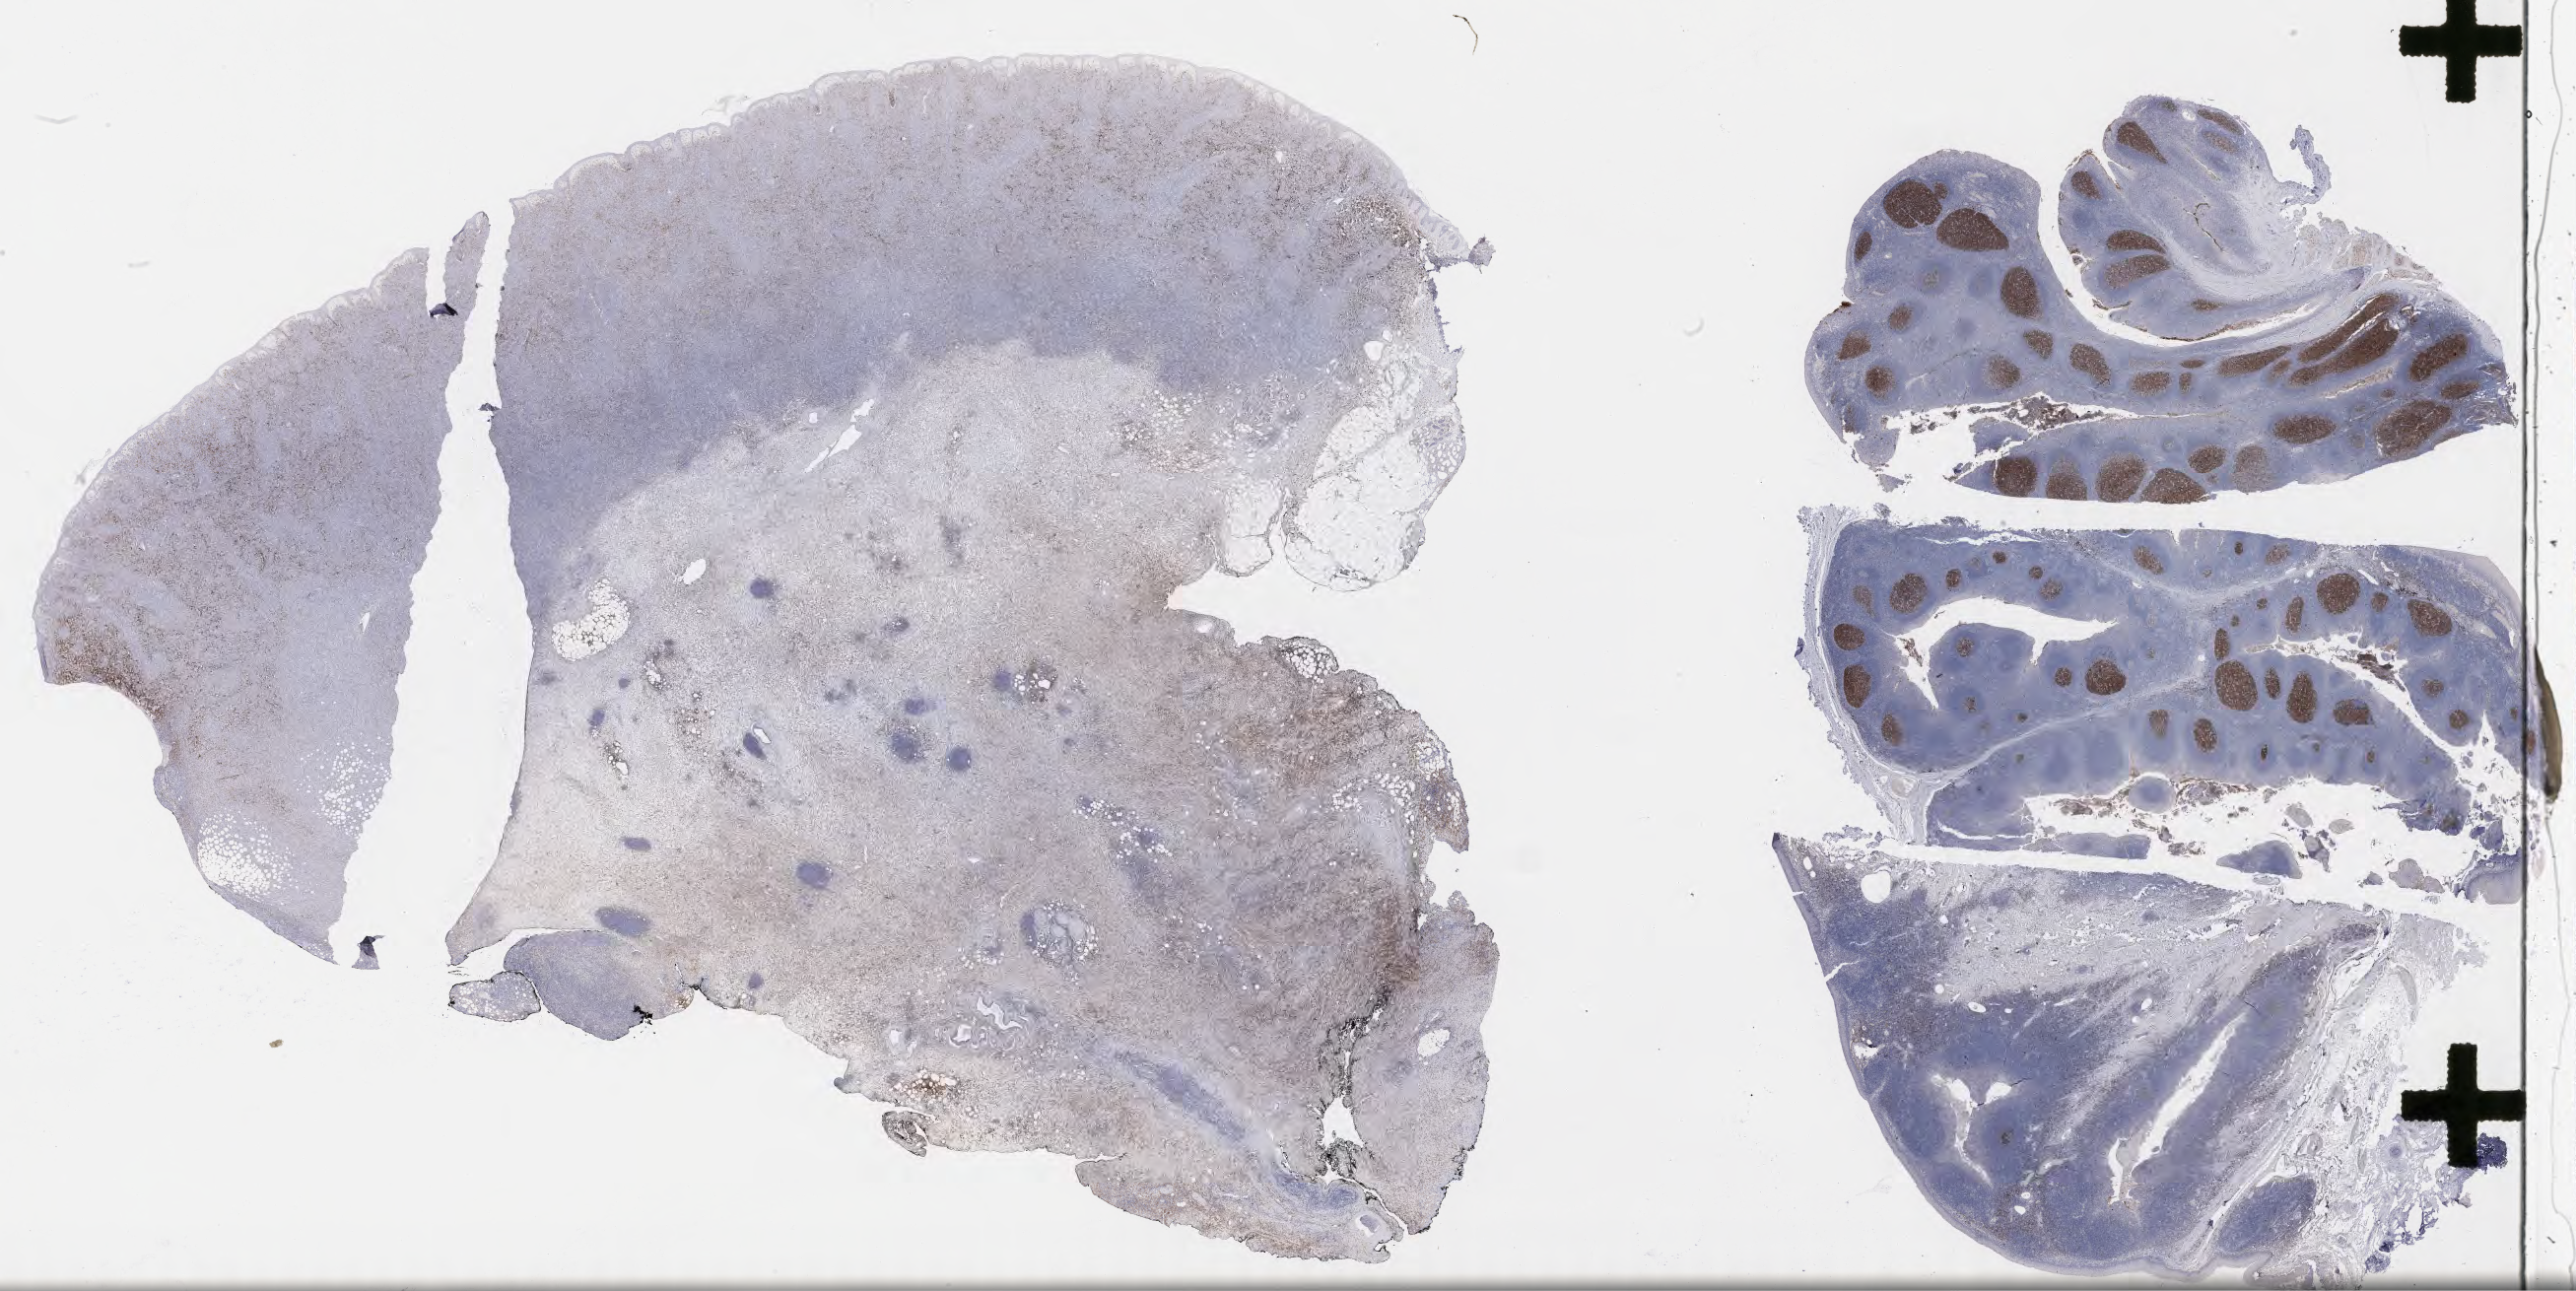
Immunohistochemistry (IHC) whole-slide image stained for CD10 — low-resolution overview of the scanned area, about 42.3 x 21.2 mm, specimen: tumor tissue, anatomic site: lymph node. Patient male; age 52 years.
Diagnosis: Diffuse large B-cell lymphoma, NOS.